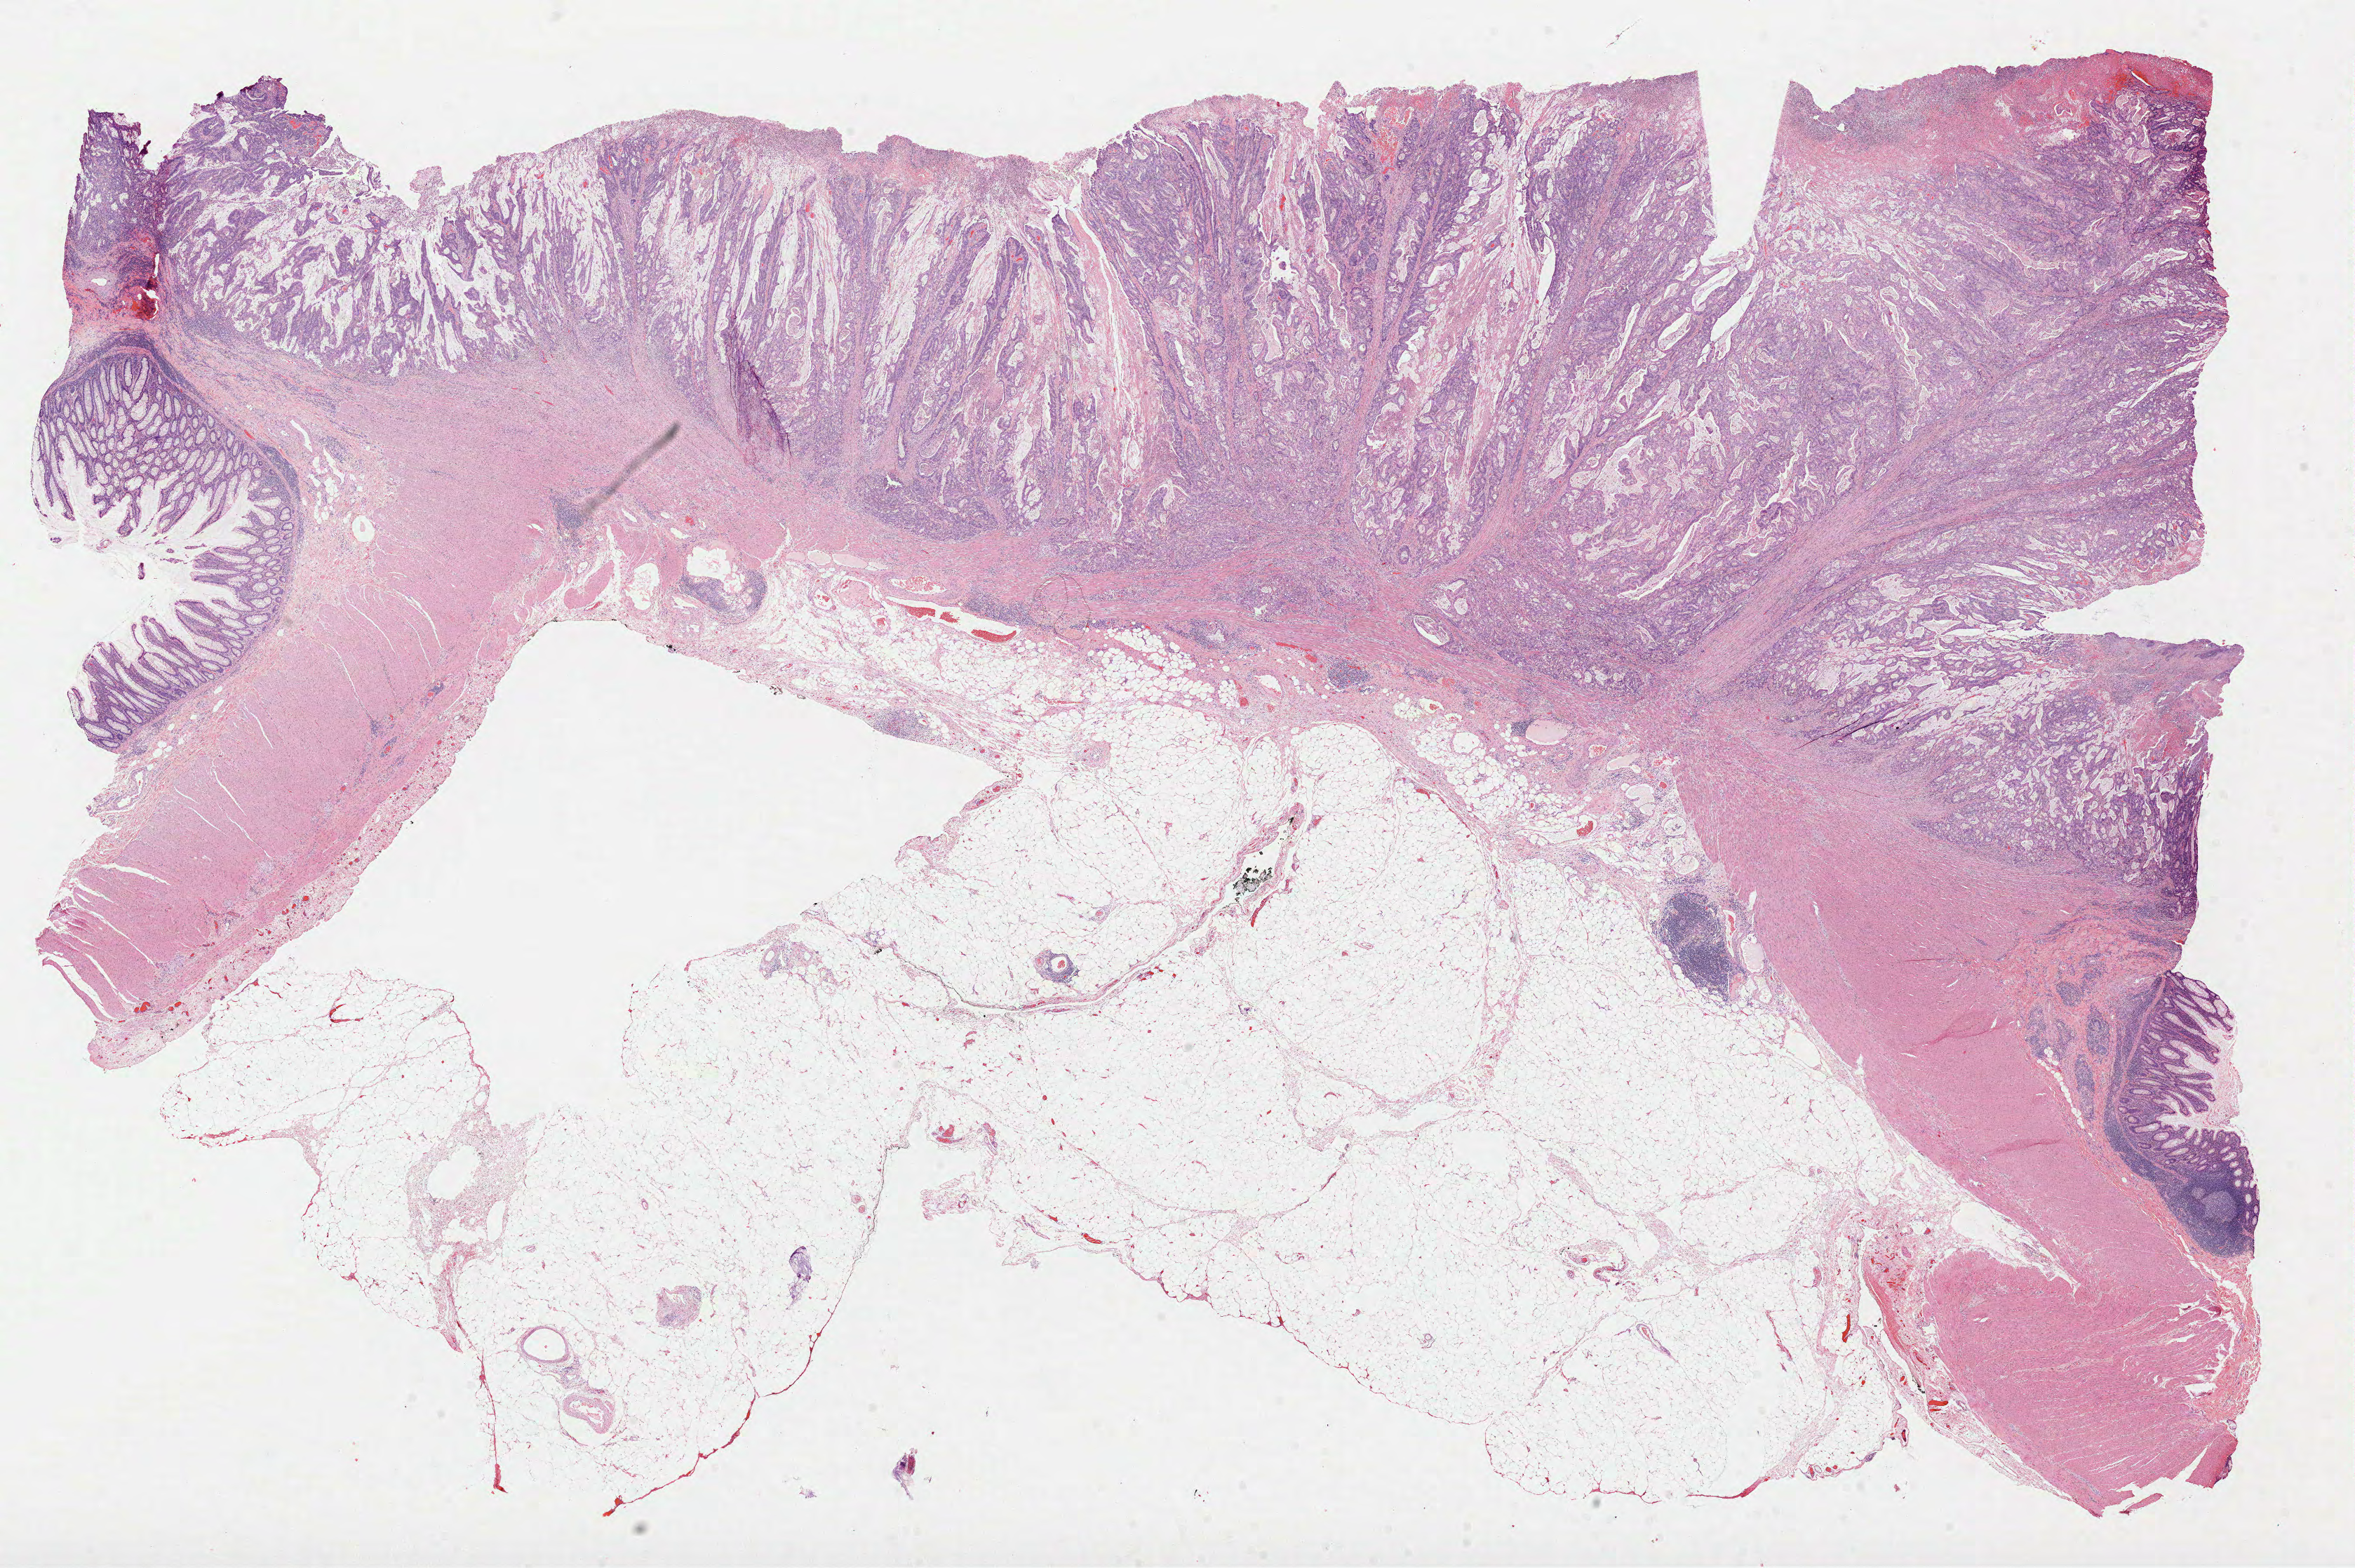
H&E whole-slide image, whole scanned area (about 27.1 x 18.0 mm, acquisition: 40x scan) shown as a low-resolution overview. FFPE section. Sample: primary tumour, colon. Female patient; age at initial diagnosis 73 years.
- lymph nodes positive (case pathology): 0 of 17 examined
- AJCC pathologic stage: IIA (6th edition)
- pathologic diagnosis: Adenocarcinoma, NOS